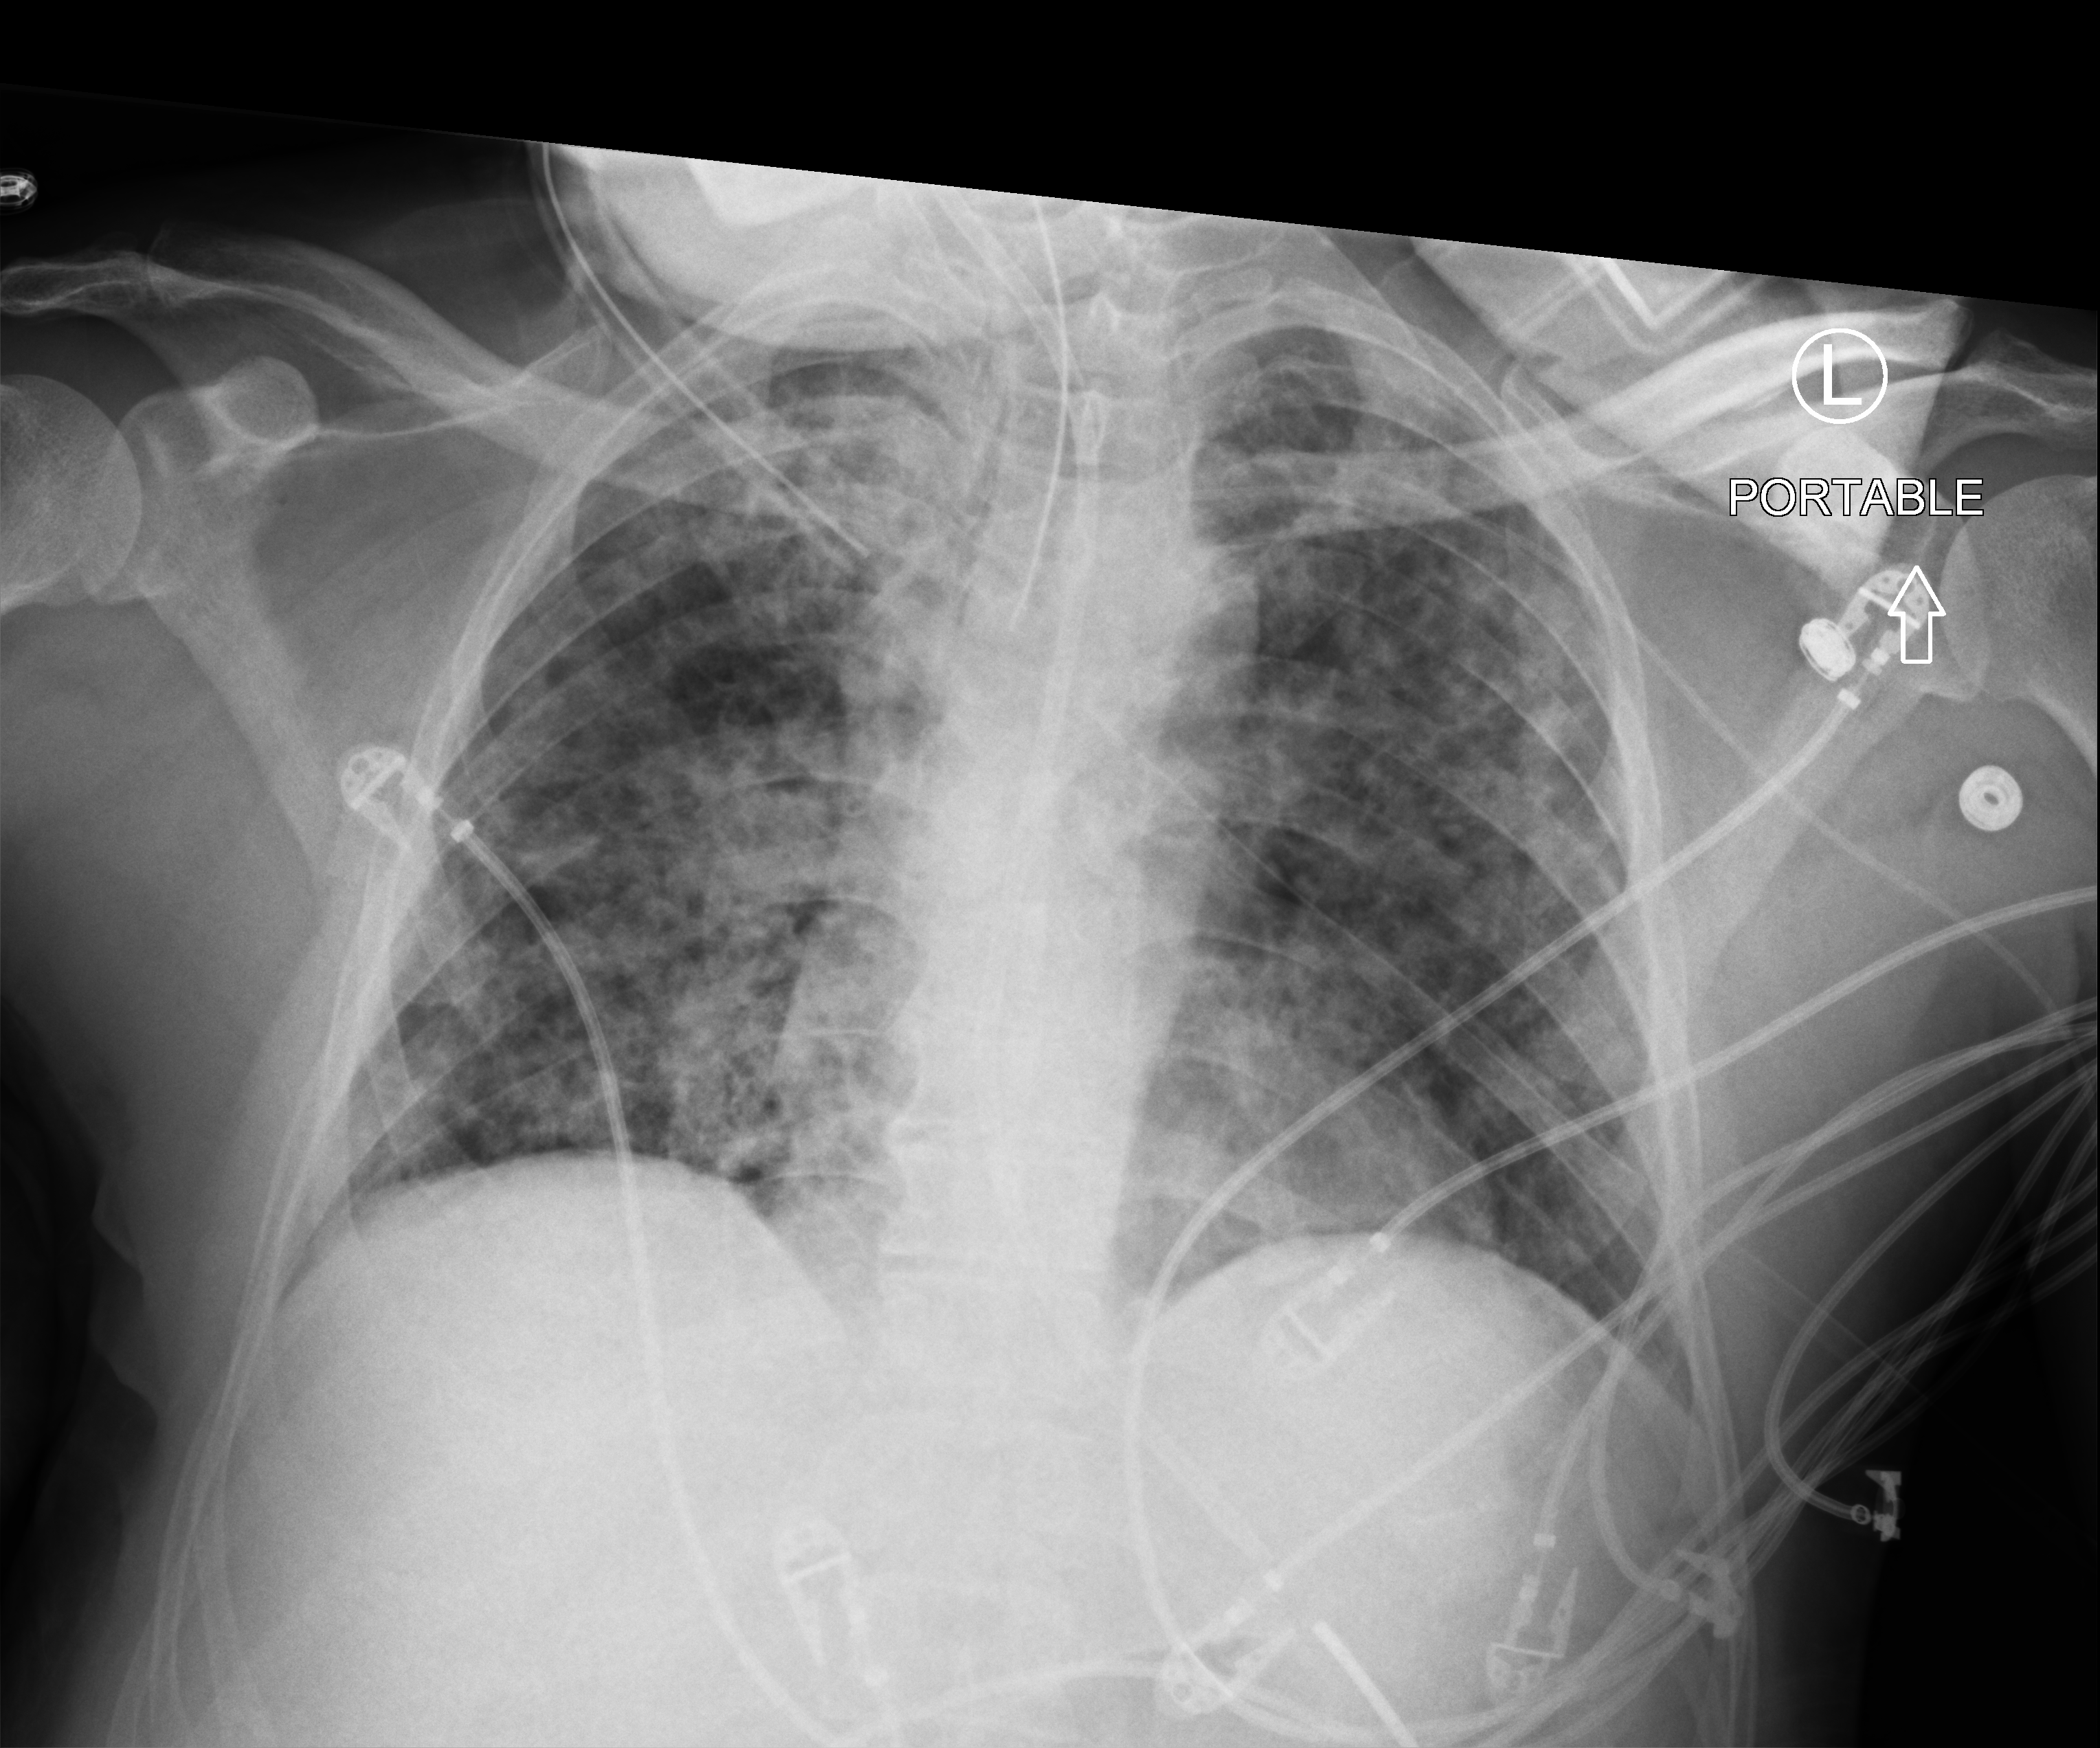
Chest X-ray (portable); anteroposterior (AP) projection. Patient hospitalised with COVID-19; male, aged 18–59 years.
Admission-level facts for this patient (not findings on this image; timing relative to this image not recorded): mechanically ventilated during this hospital stay: yes.